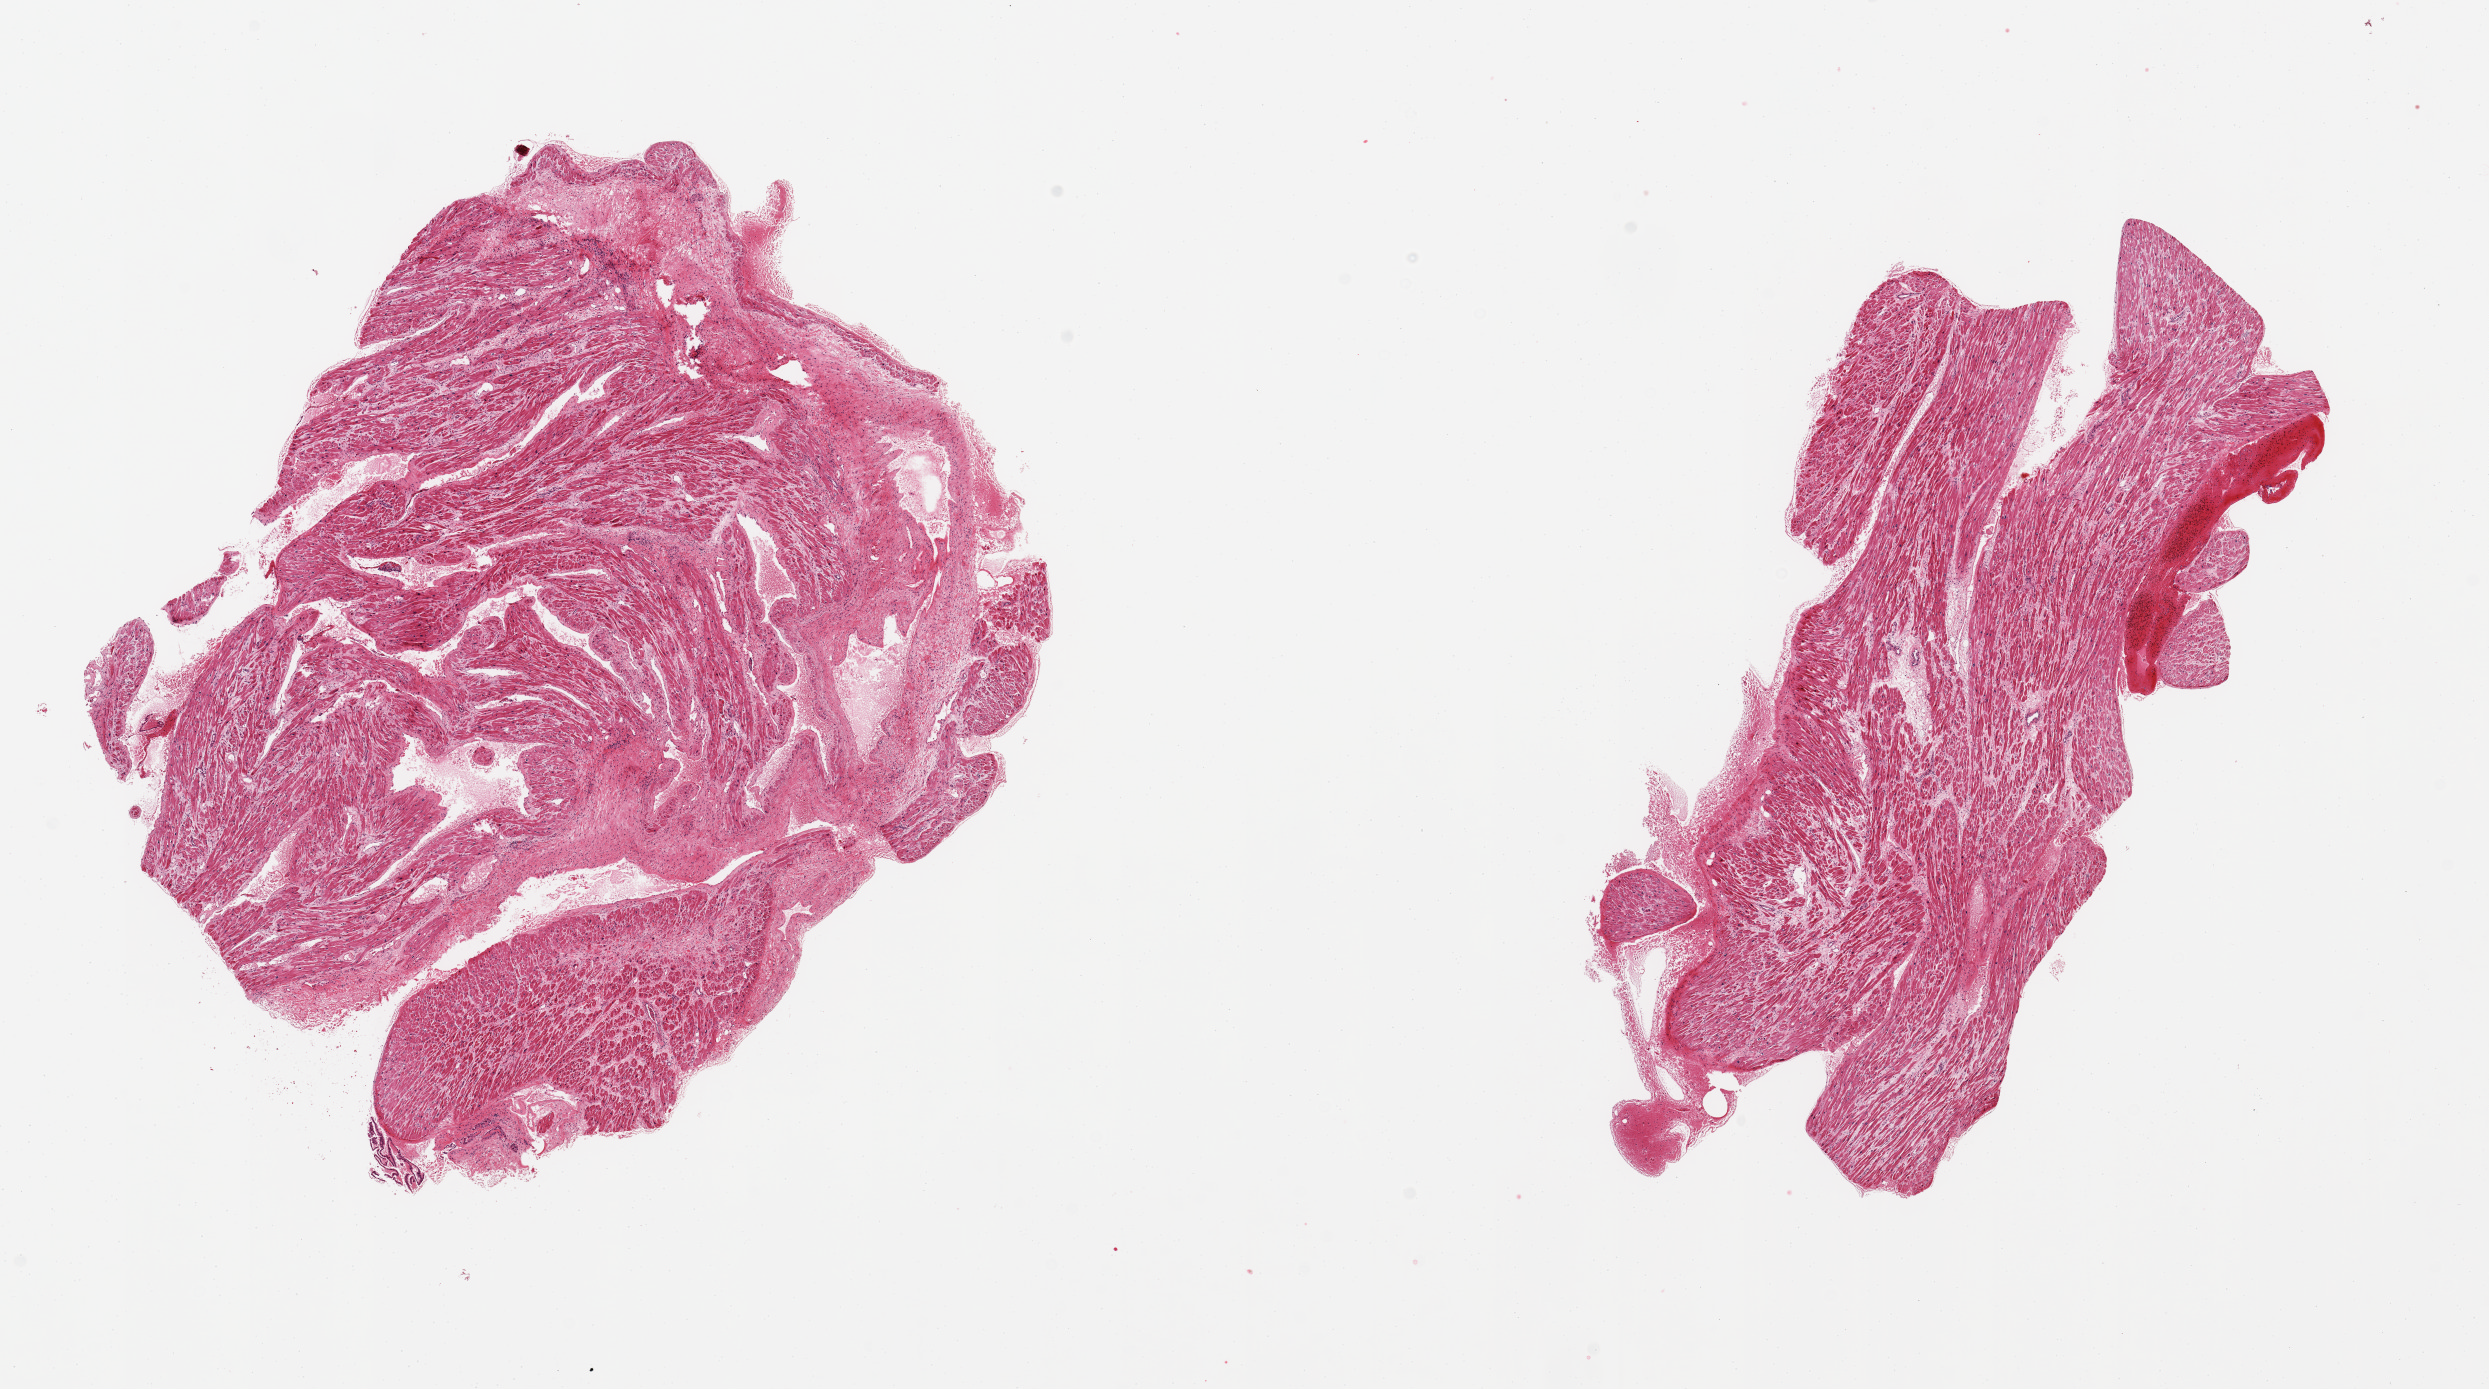
Digitized haematoxylin and eosin-stained section, whole scanned area (about 19.7 x 11.0 mm, from a 20x scan) shown as a low-resolution overview, PAXgene-fixed, paraffin-embedded tissue, sampled site (target tissue): auricular appendage, tissue donor sample. Female donor.
• pathologist's review note for this sample: 2 pieces, no abnormalities